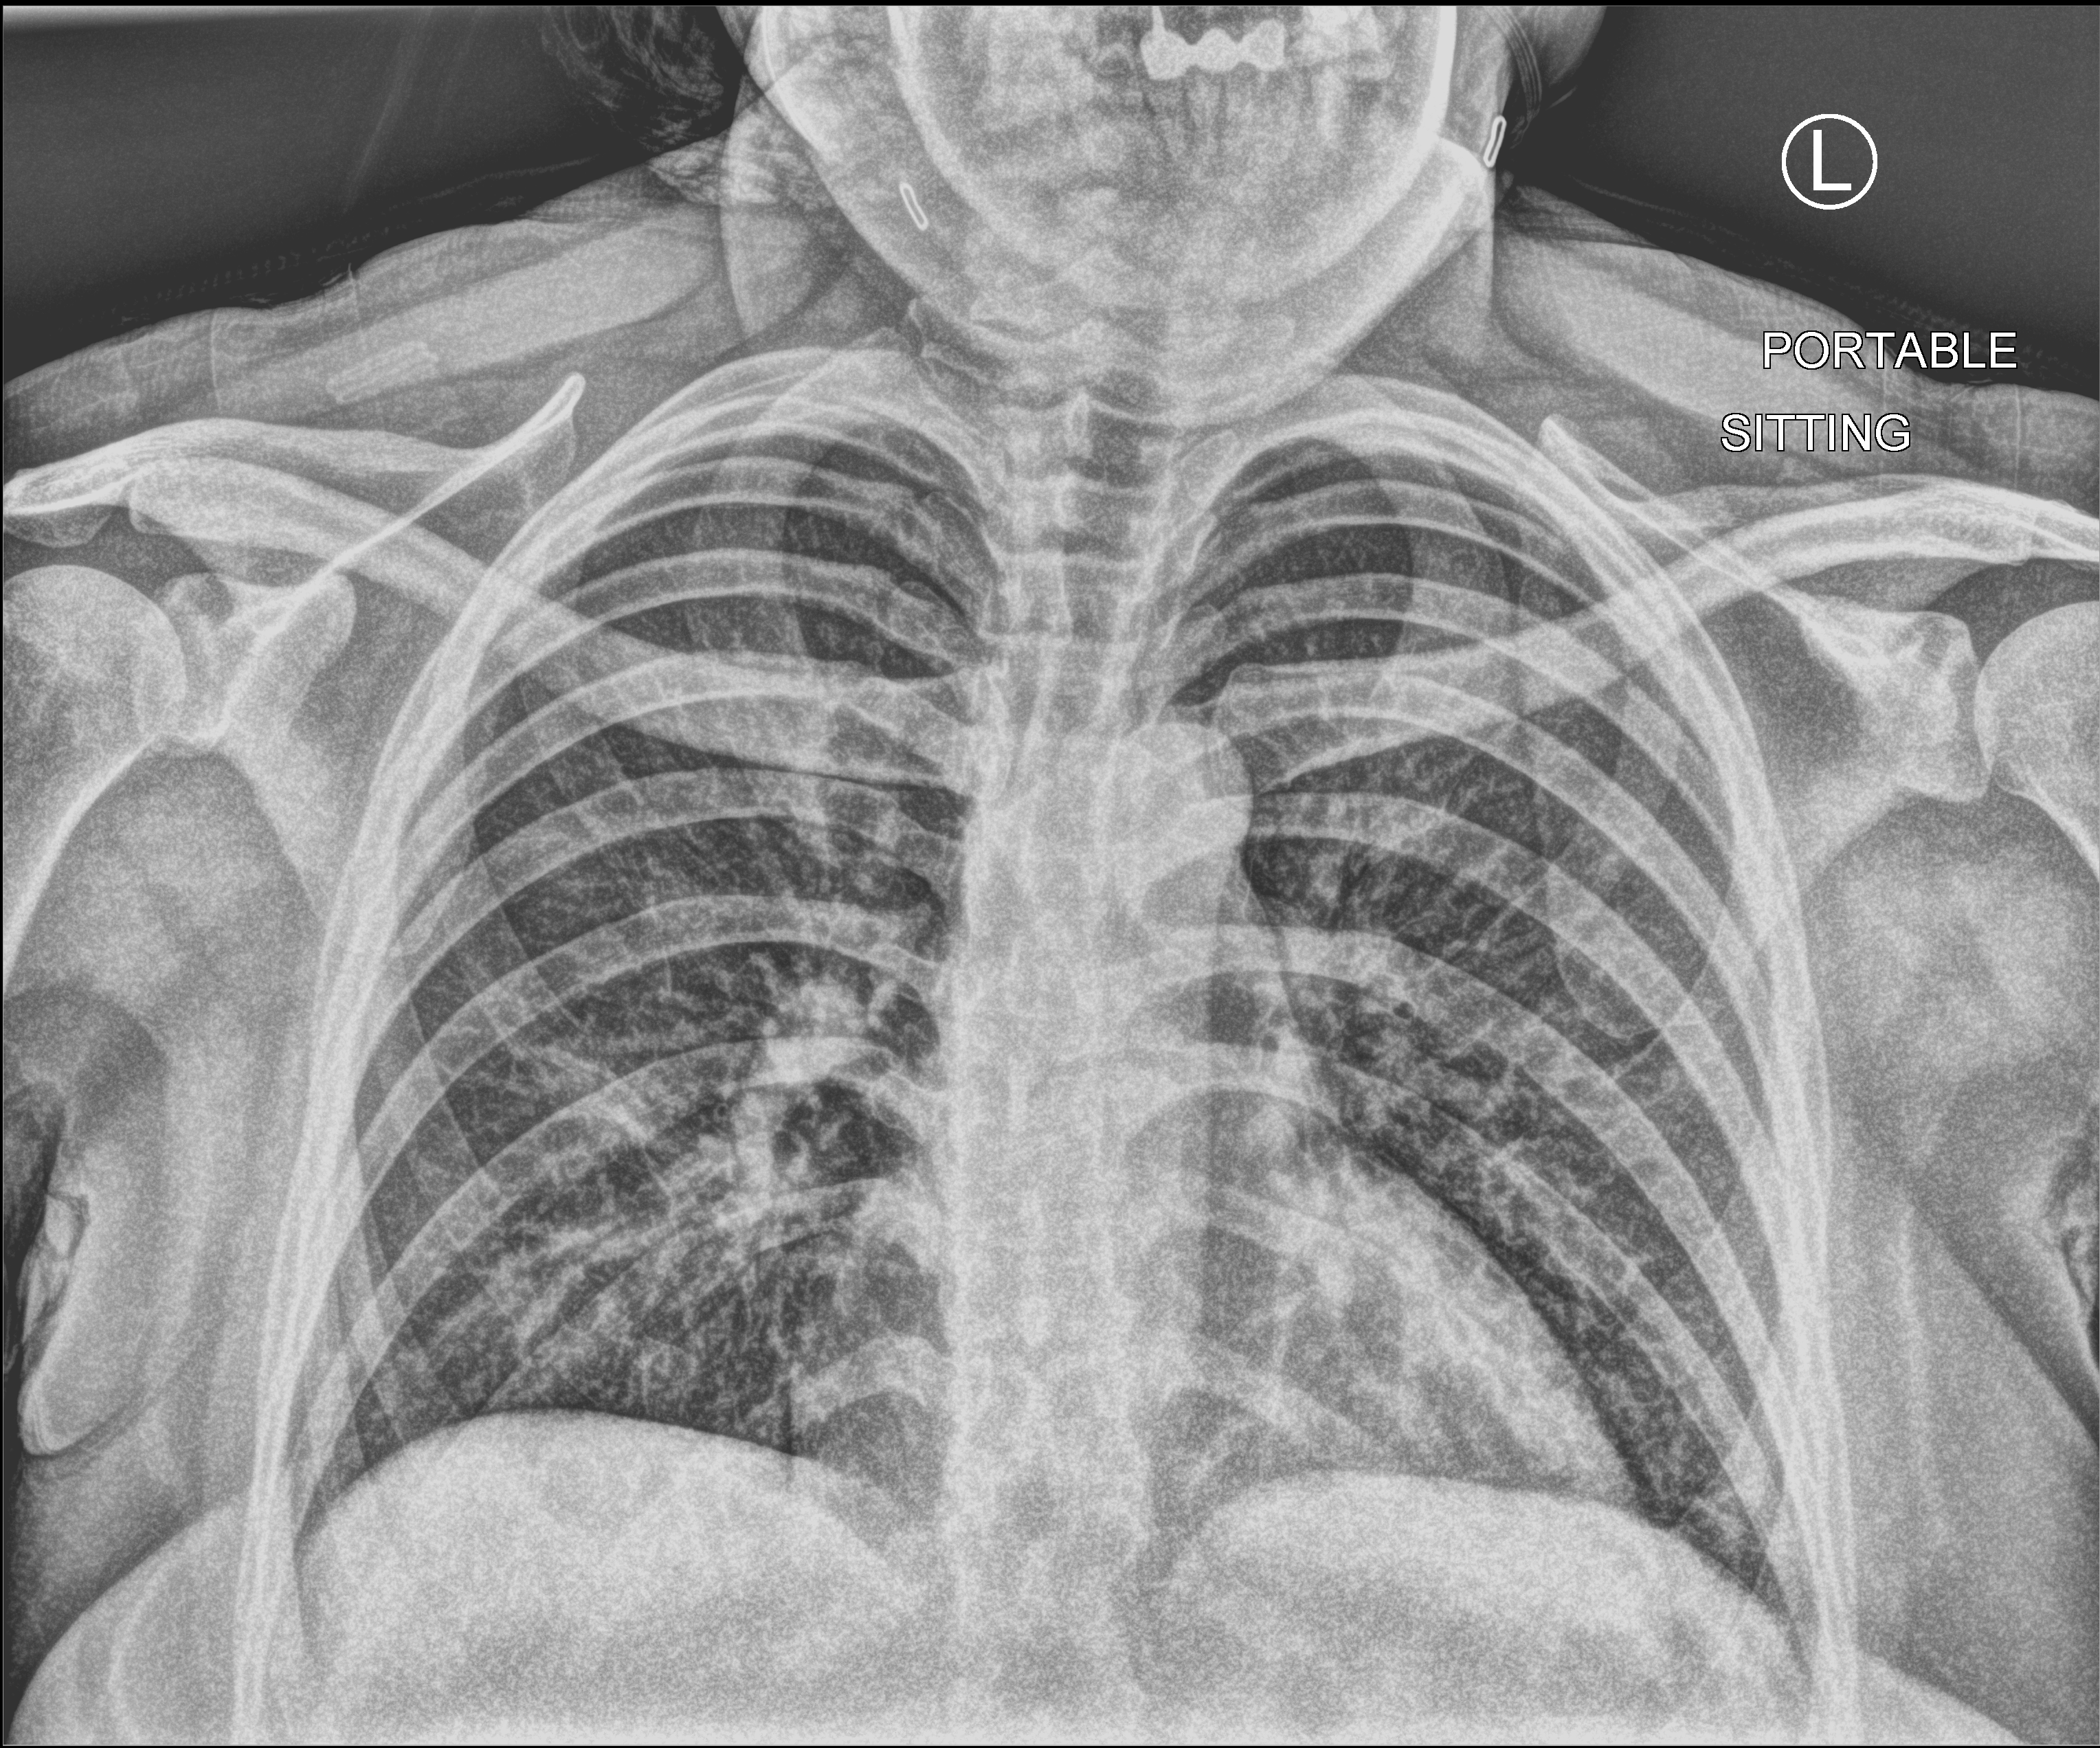
Portable chest radiograph, anteroposterior (AP) projection. Female patient hospitalised with COVID-19, age 18–59 years.
Admission-level facts for this patient (not findings on this image; timing relative to this image not recorded):
- admitted to intensive care during this hospital stay: no
- mechanically ventilated during this hospital stay: no
- chronic kidney disease (admission record): no